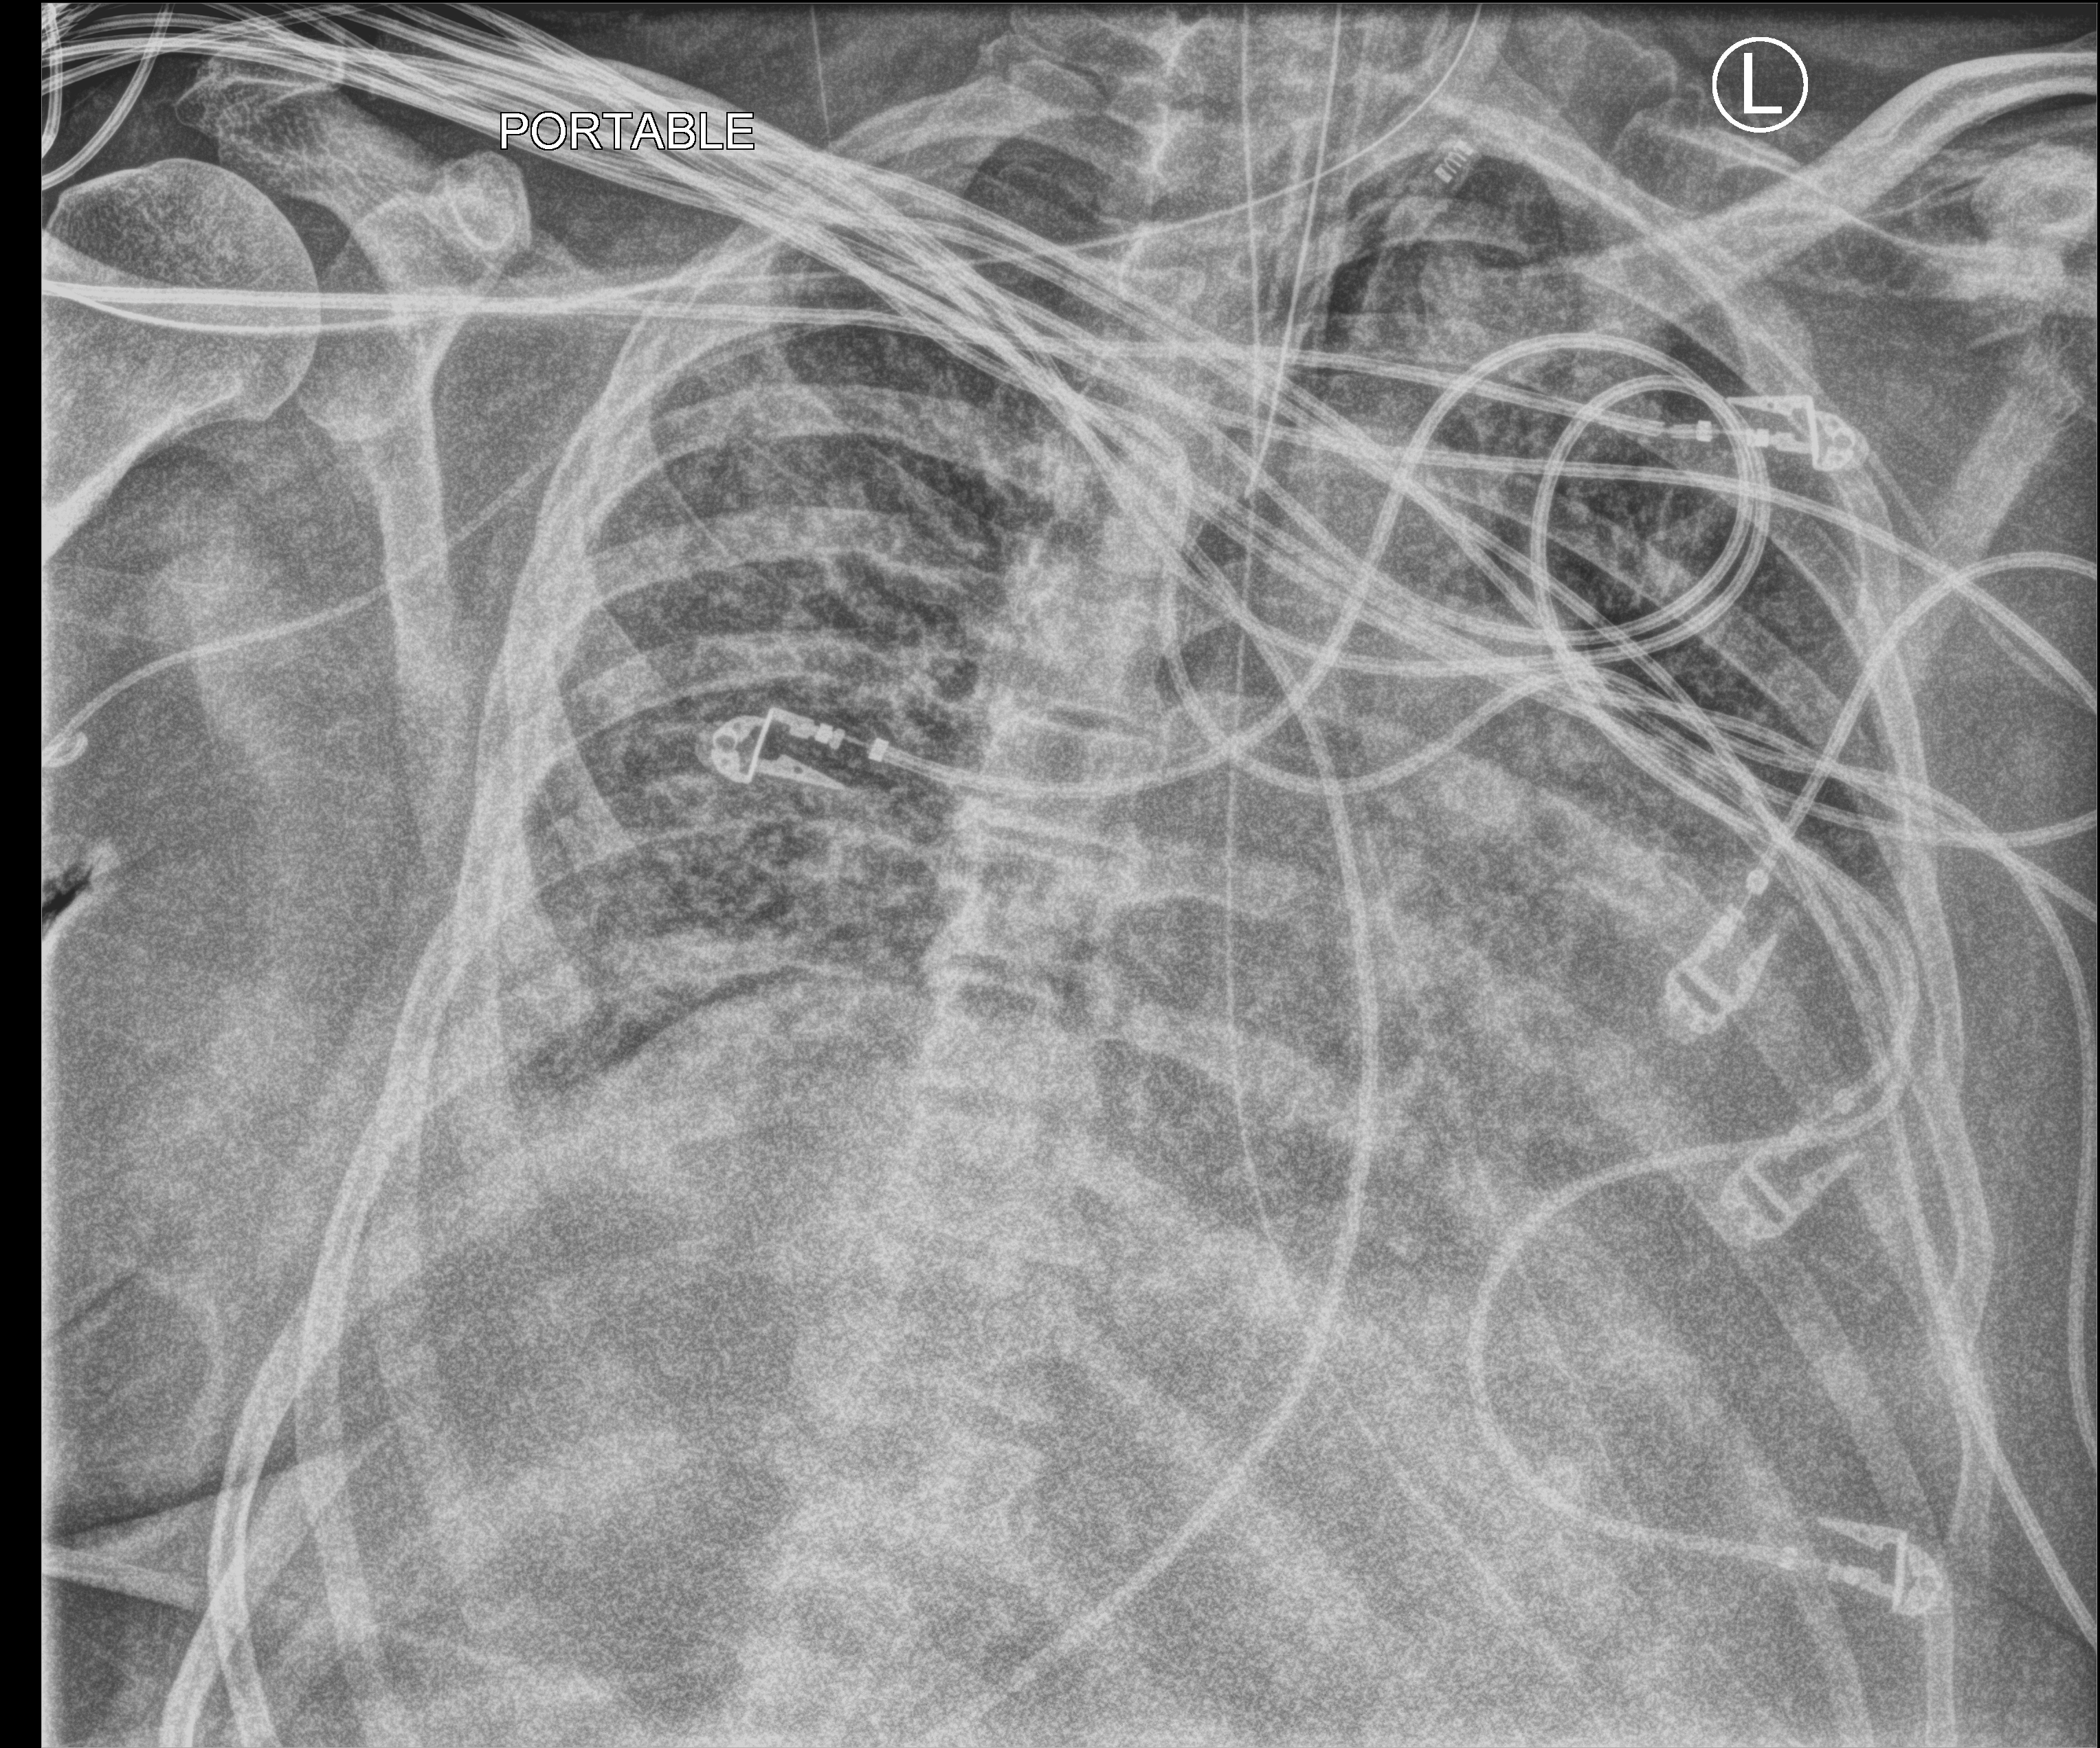
Portable chest radiograph, anteroposterior (AP) projection. Patient hospitalised with COVID-19; male, aged 60–74 years.
Hospital-stay facts (about this admission, not read from this image; timing relative to this image not recorded): admitted to intensive care during this hospital stay: yes.